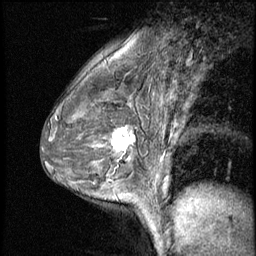
Breast MRI (dynamic contrast-enhanced), one sagittal slice. Position 39 of 56 along the scan axis. 3 images stored at this slice position (order not interpretable as contrast timing). 1.5 T. TE 4.2 ms, TR 8.7 ms. 2.5 mm slice thickness. 256 × 256 image matrix. Female patient, age 43 years. Case-level facts recorded for this patient, not image findings: setting: breast cancer imaged before/during neoadjuvant chemotherapy; receptor status: HR-positive, HER2-negative.
Outlined on this slice (semi-automatic segmentation, software-assisted and operator-edited):
- analysis volume of interest (the breast-tissue region the enhancement analysis was run in; not a lesion): bounding box <101,120,145,165> (left, top, right, bottom; pixels)
- tumour enhancement mask (voxels above the 140 % enhancement threshold inside the analysis volume of interest): <113,128,135,151>